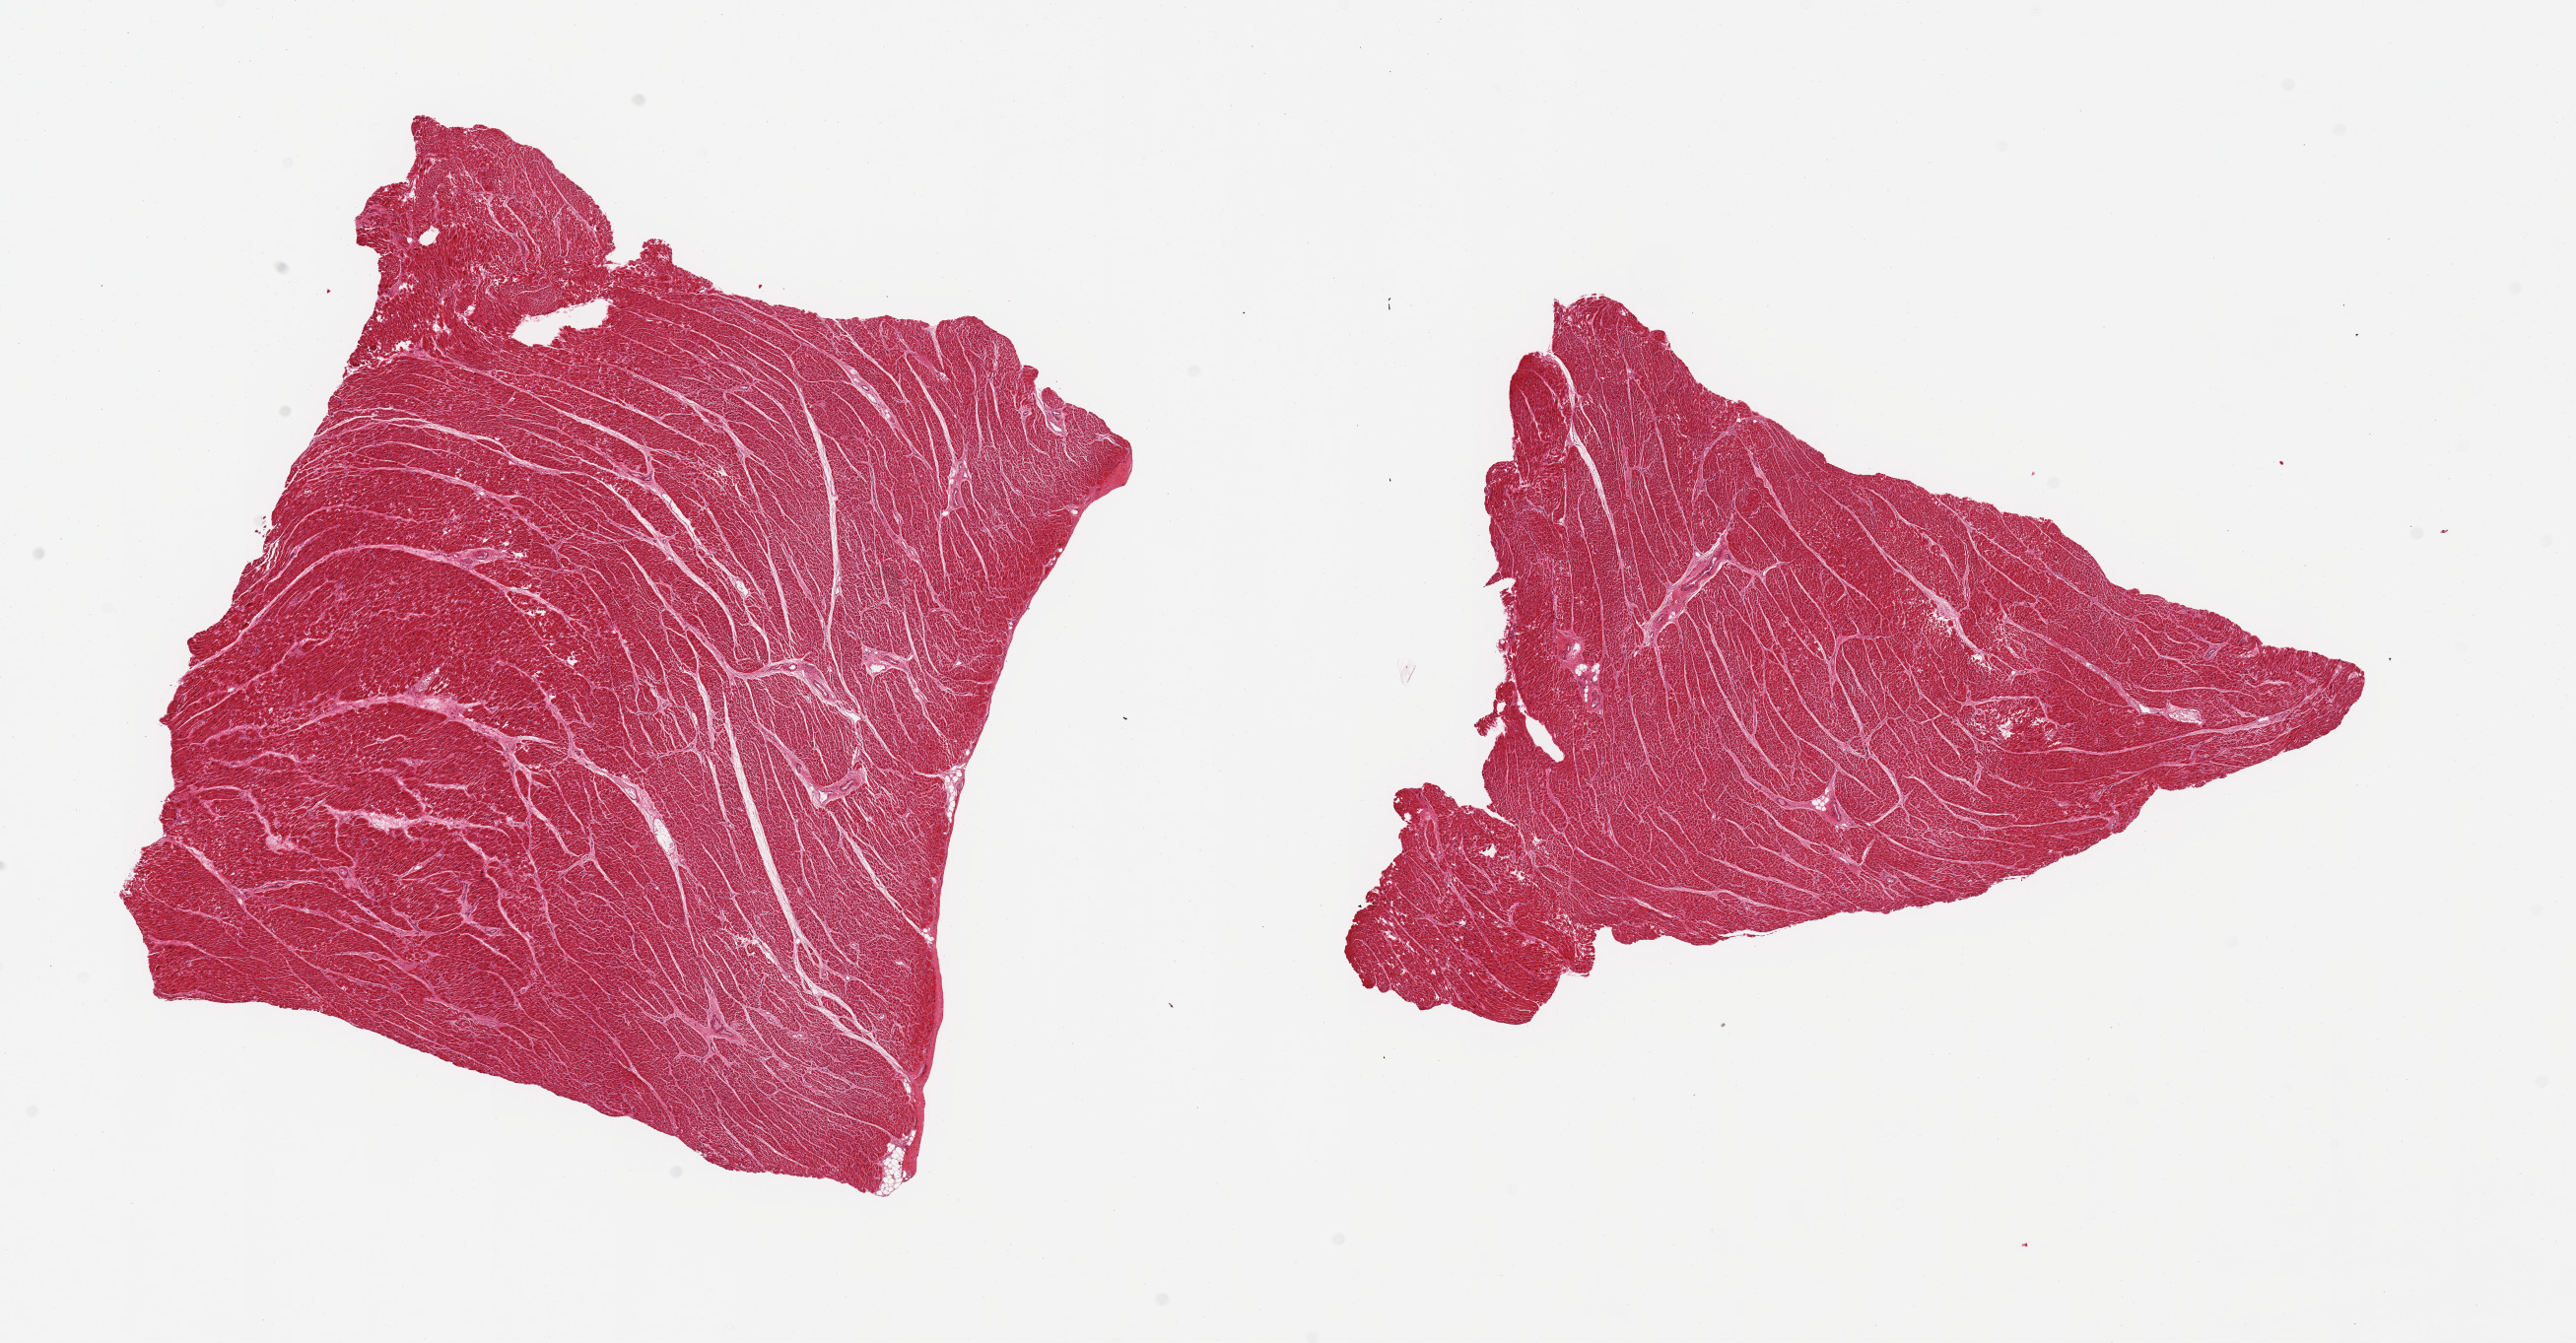
Hematoxylin and eosin (H&E) whole-slide image, brightfield — shown as a low-resolution overview of the whole scanned area (about 20.7 x 10.8 mm), PAXgene-fixed paraffin-embedded (PFPE) section, target tissue: heart, donor tissue sample. Donor sex: female.
Review note (as recorded): 2 pieces, minimal interstitial fibrosis/chronic ischemic damage.